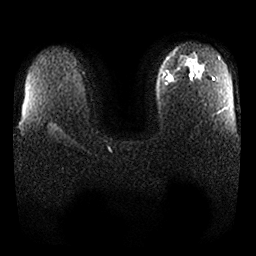
Breast MRI, one axial slice; slice 19 of 25 in the series (ordered by position); diffusion-weighted series; image 2 of 4 stored at this slice position (different b-values; order by instance number); 1.5 T; 4 mm slice thickness; 256 × 256 image matrix, field of view 340 × 340 mm. Female patient.
Outlined on this slice (expert manual segmentation):
- tumour on diffusion-weighted imaging: bounding box <165,74,174,82> (left, top, right, bottom; pixels)